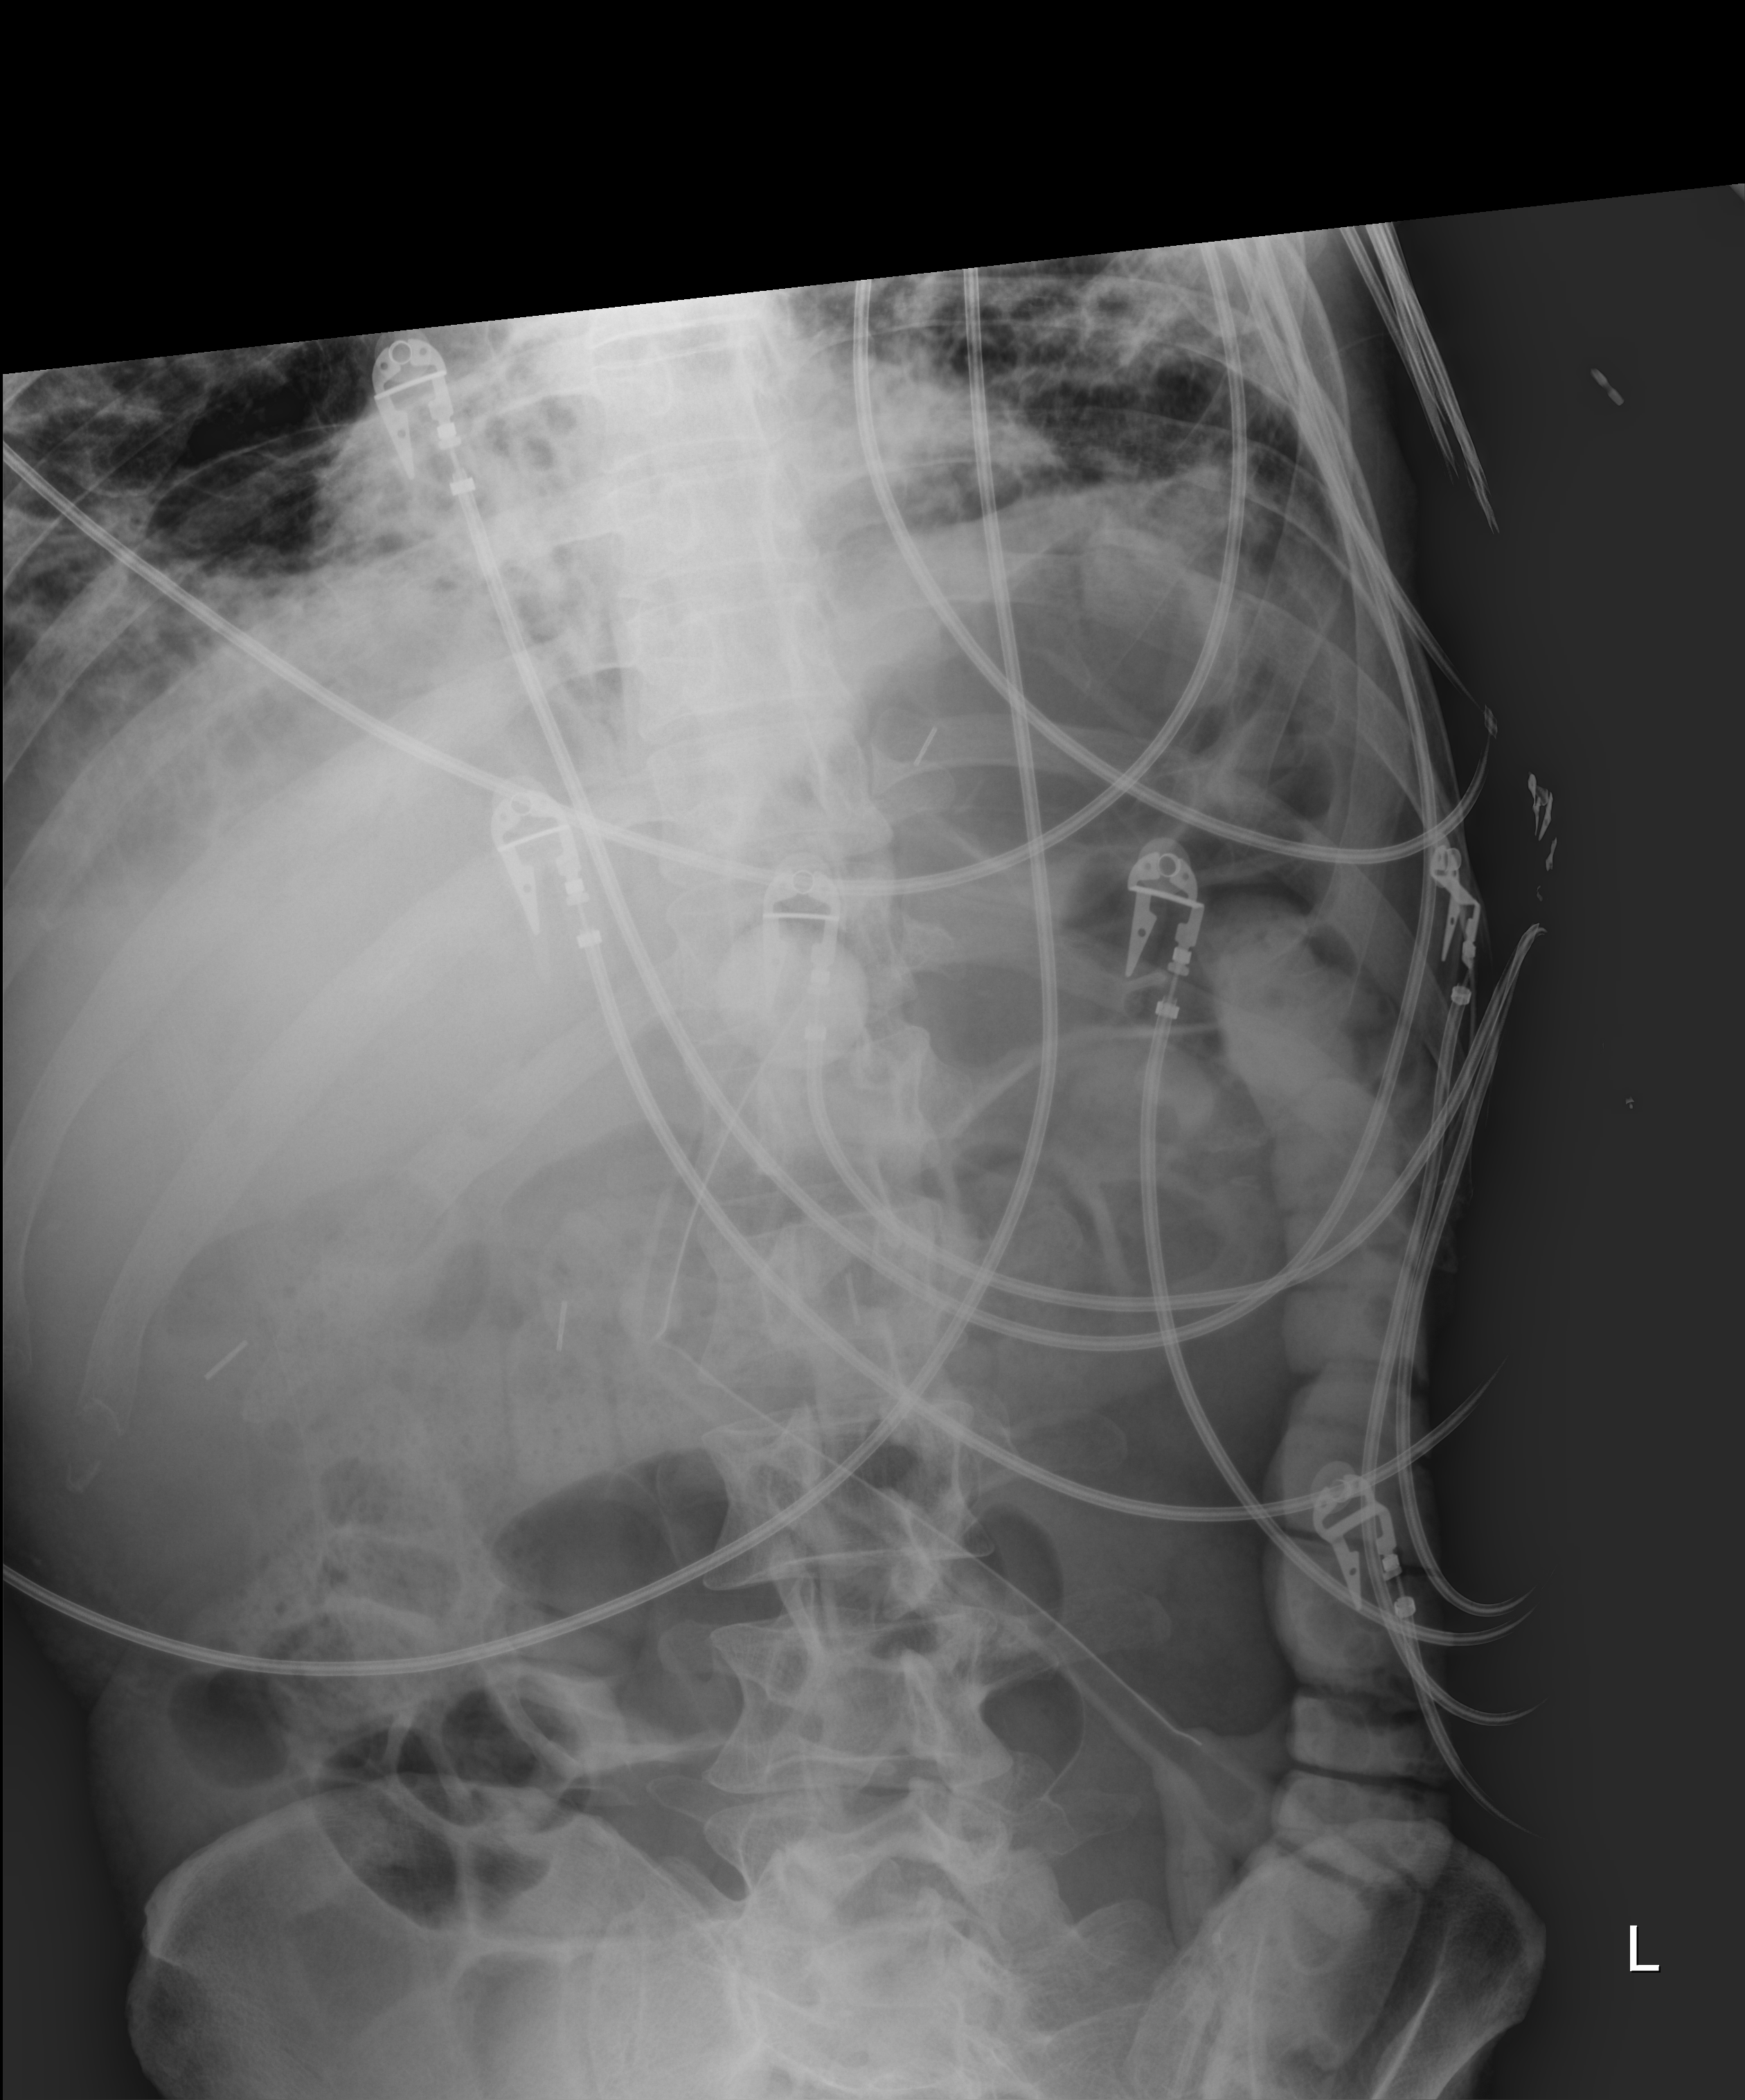
Bedside abdomen radiograph (digital radiography); anteroposterior (AP) projection. Male patient hospitalised with COVID-19, age 18–59 years.
Hospital-stay facts (about this admission, not read from this image; timing relative to this image not recorded):
- other chronic lung disease (admission record): no